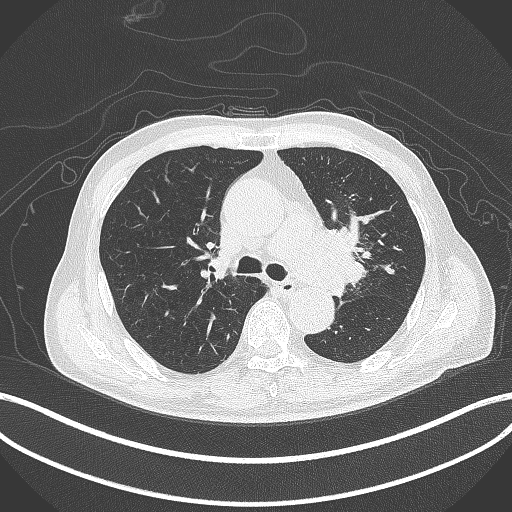
Chest CT, one axial slice; position 280 of 417 along the scan axis; reconstruction kernel B70f; 120 kVp; lung window (W 1500 / L -600 HU); 1 mm slice thickness; 512 × 512 image matrix. Male patient, age 77 years. From the clinical record (not read from this slice): clinical TNM (as recorded): T3 N1 M0.
Annotated regions visible in this slice (bounding box drawn by a radiologist):
- lung tumour (recorded histology: adenocarcinoma): bounding box [x1, y1, x2, y2] px = [314, 222, 366, 298]